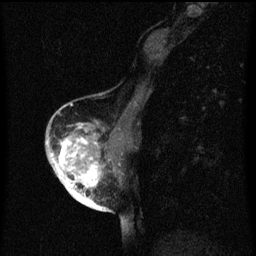
Breast MRI (dynamic contrast-enhanced), one sagittal slice. Slice 28 of 60 in the series (ordered by position). Dynamic contrast-enhanced series, image 2 of 3 at this slice position (ordered by acquisition). 1.5 T. TE 4.2 ms, TR 8 ms. 2 mm slice thickness. 256 × 256 image matrix. Patient: female, 56 years.
Outlined on this slice (semi-automatic segmentation, software-assisted and operator-edited):
- analysis volume of interest (the breast-tissue region the enhancement analysis was run in; not a lesion): bounding box [x1, y1, x2, y2] px = [54, 122, 120, 199]
- tumour enhancement mask (voxels above the 70 % enhancement threshold inside the analysis volume of interest): [54, 128, 100, 199]